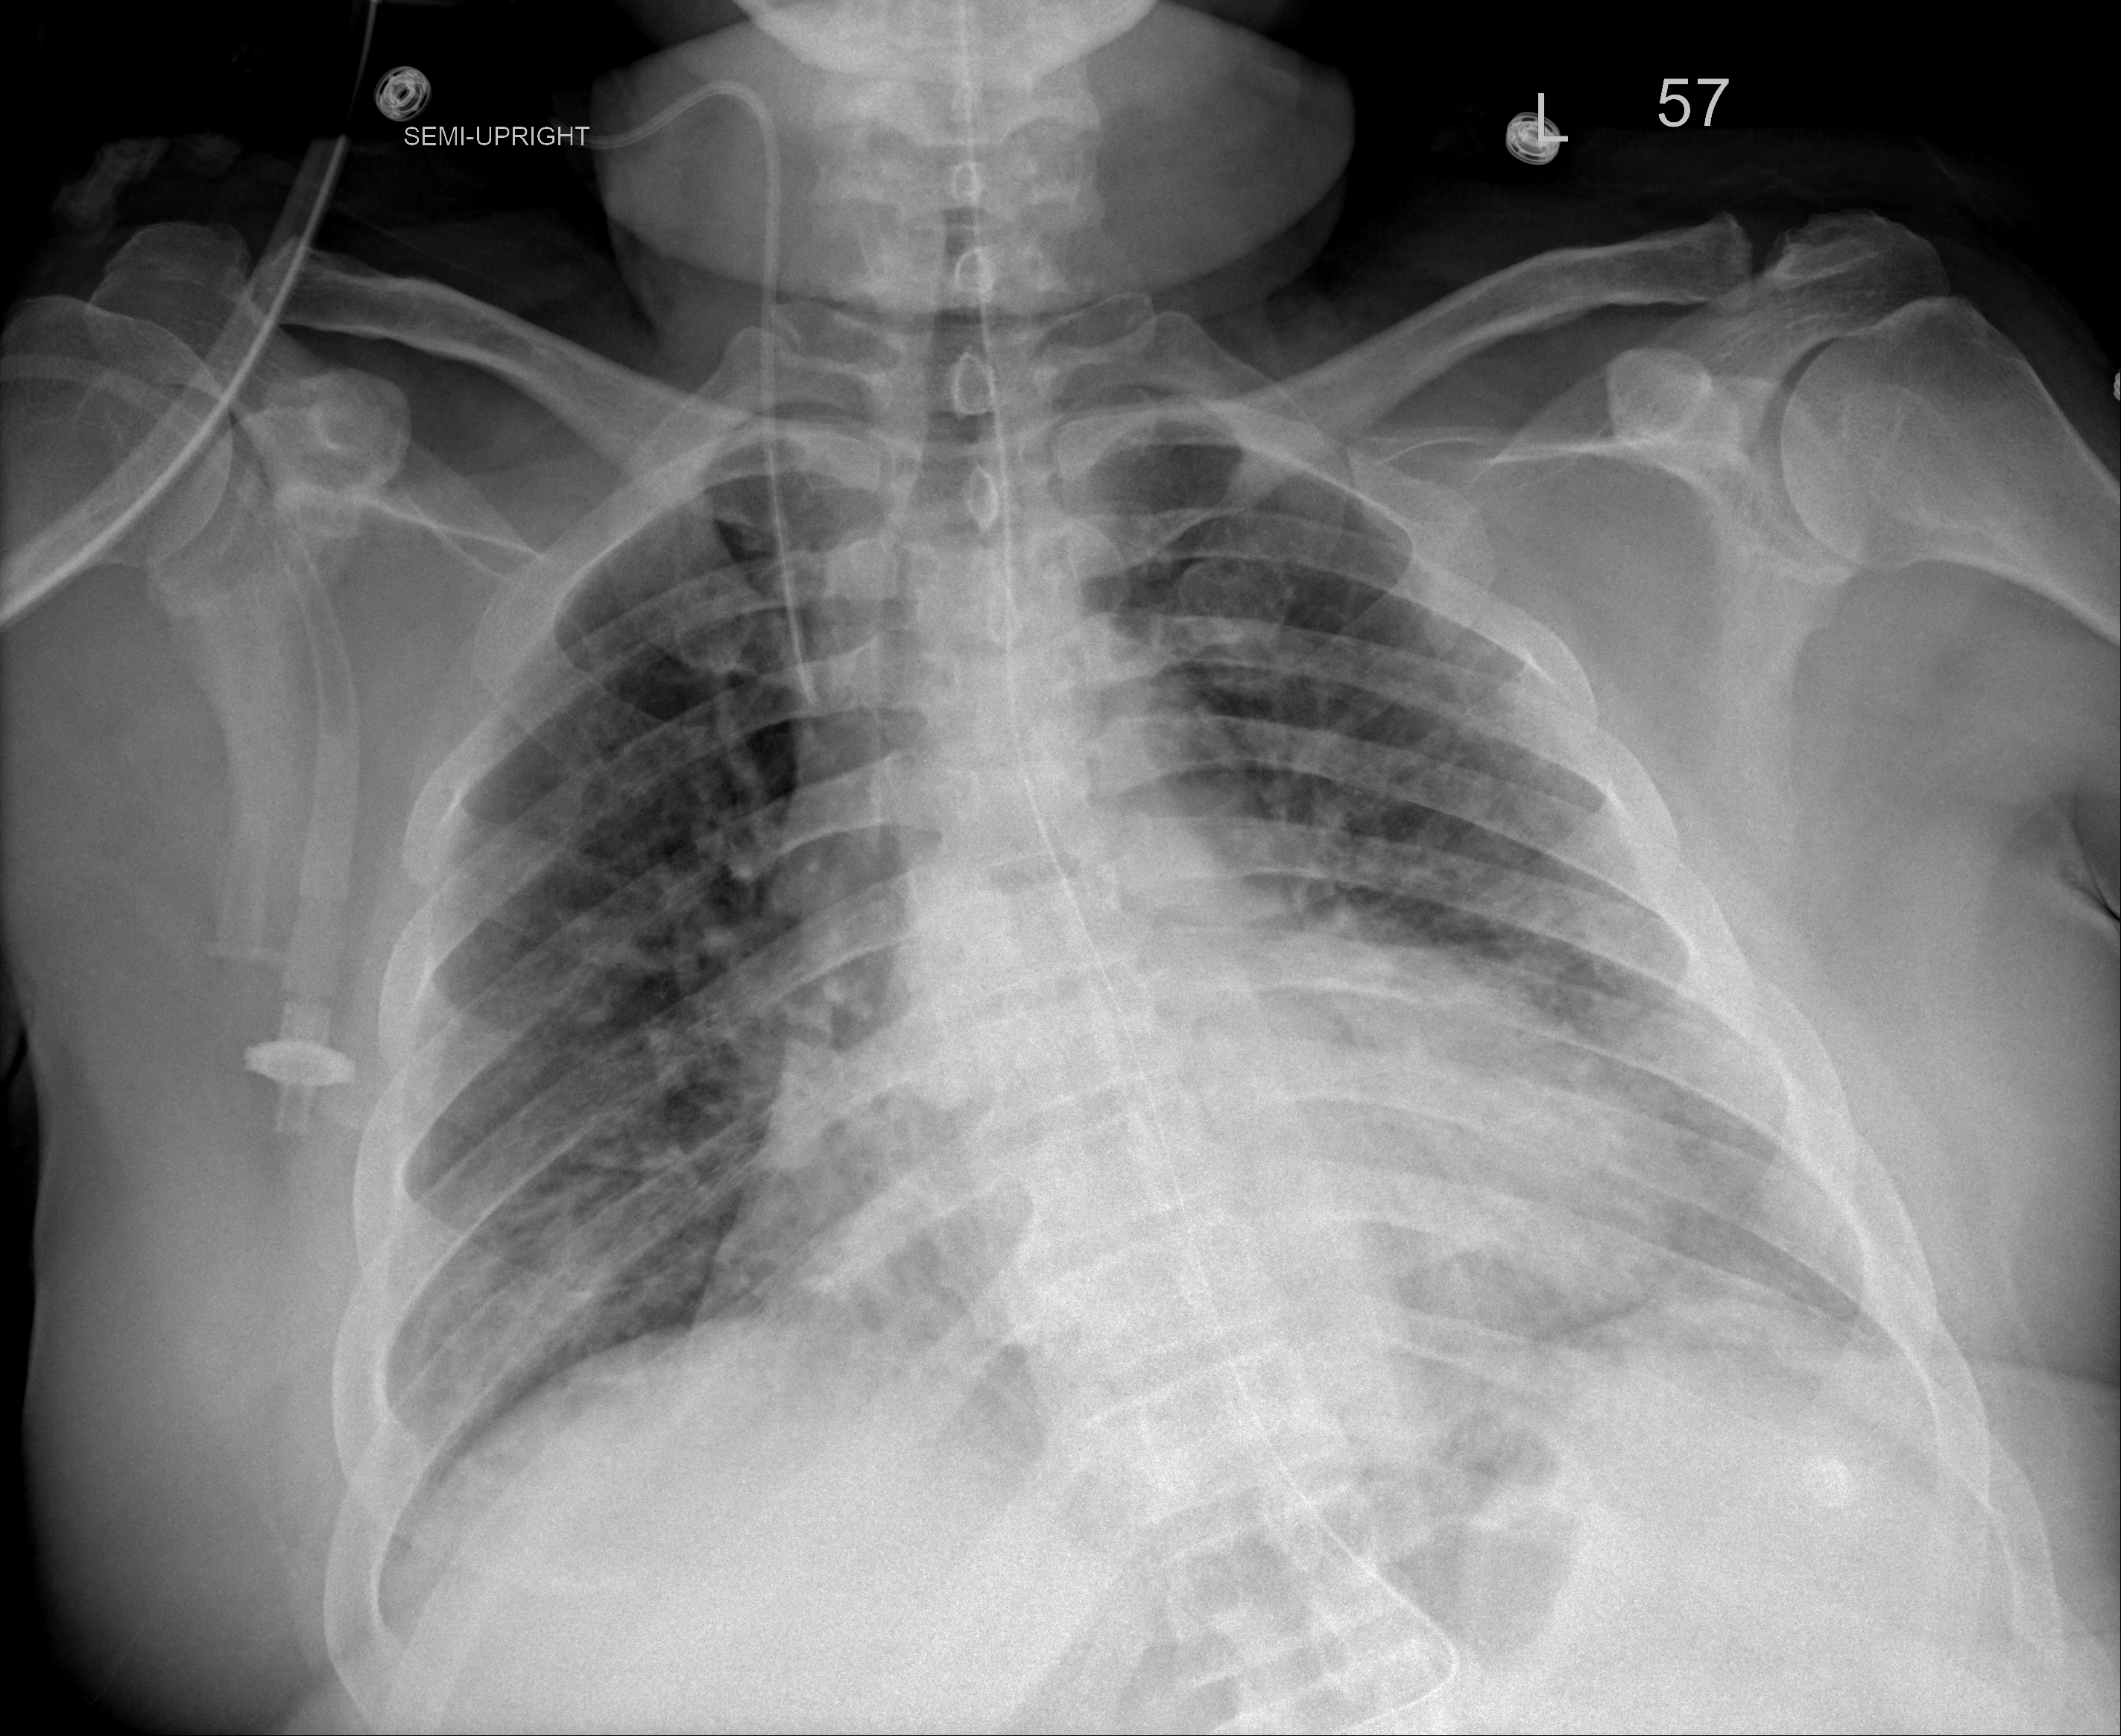
Chest X-ray (portable), AP projection. Male patient, age 55 years; imaged 21 days after the COVID-19 diagnosis.
Key findings recorded by the radiologist: Residual ill-defined bibasilar opacities, not significantly changed.